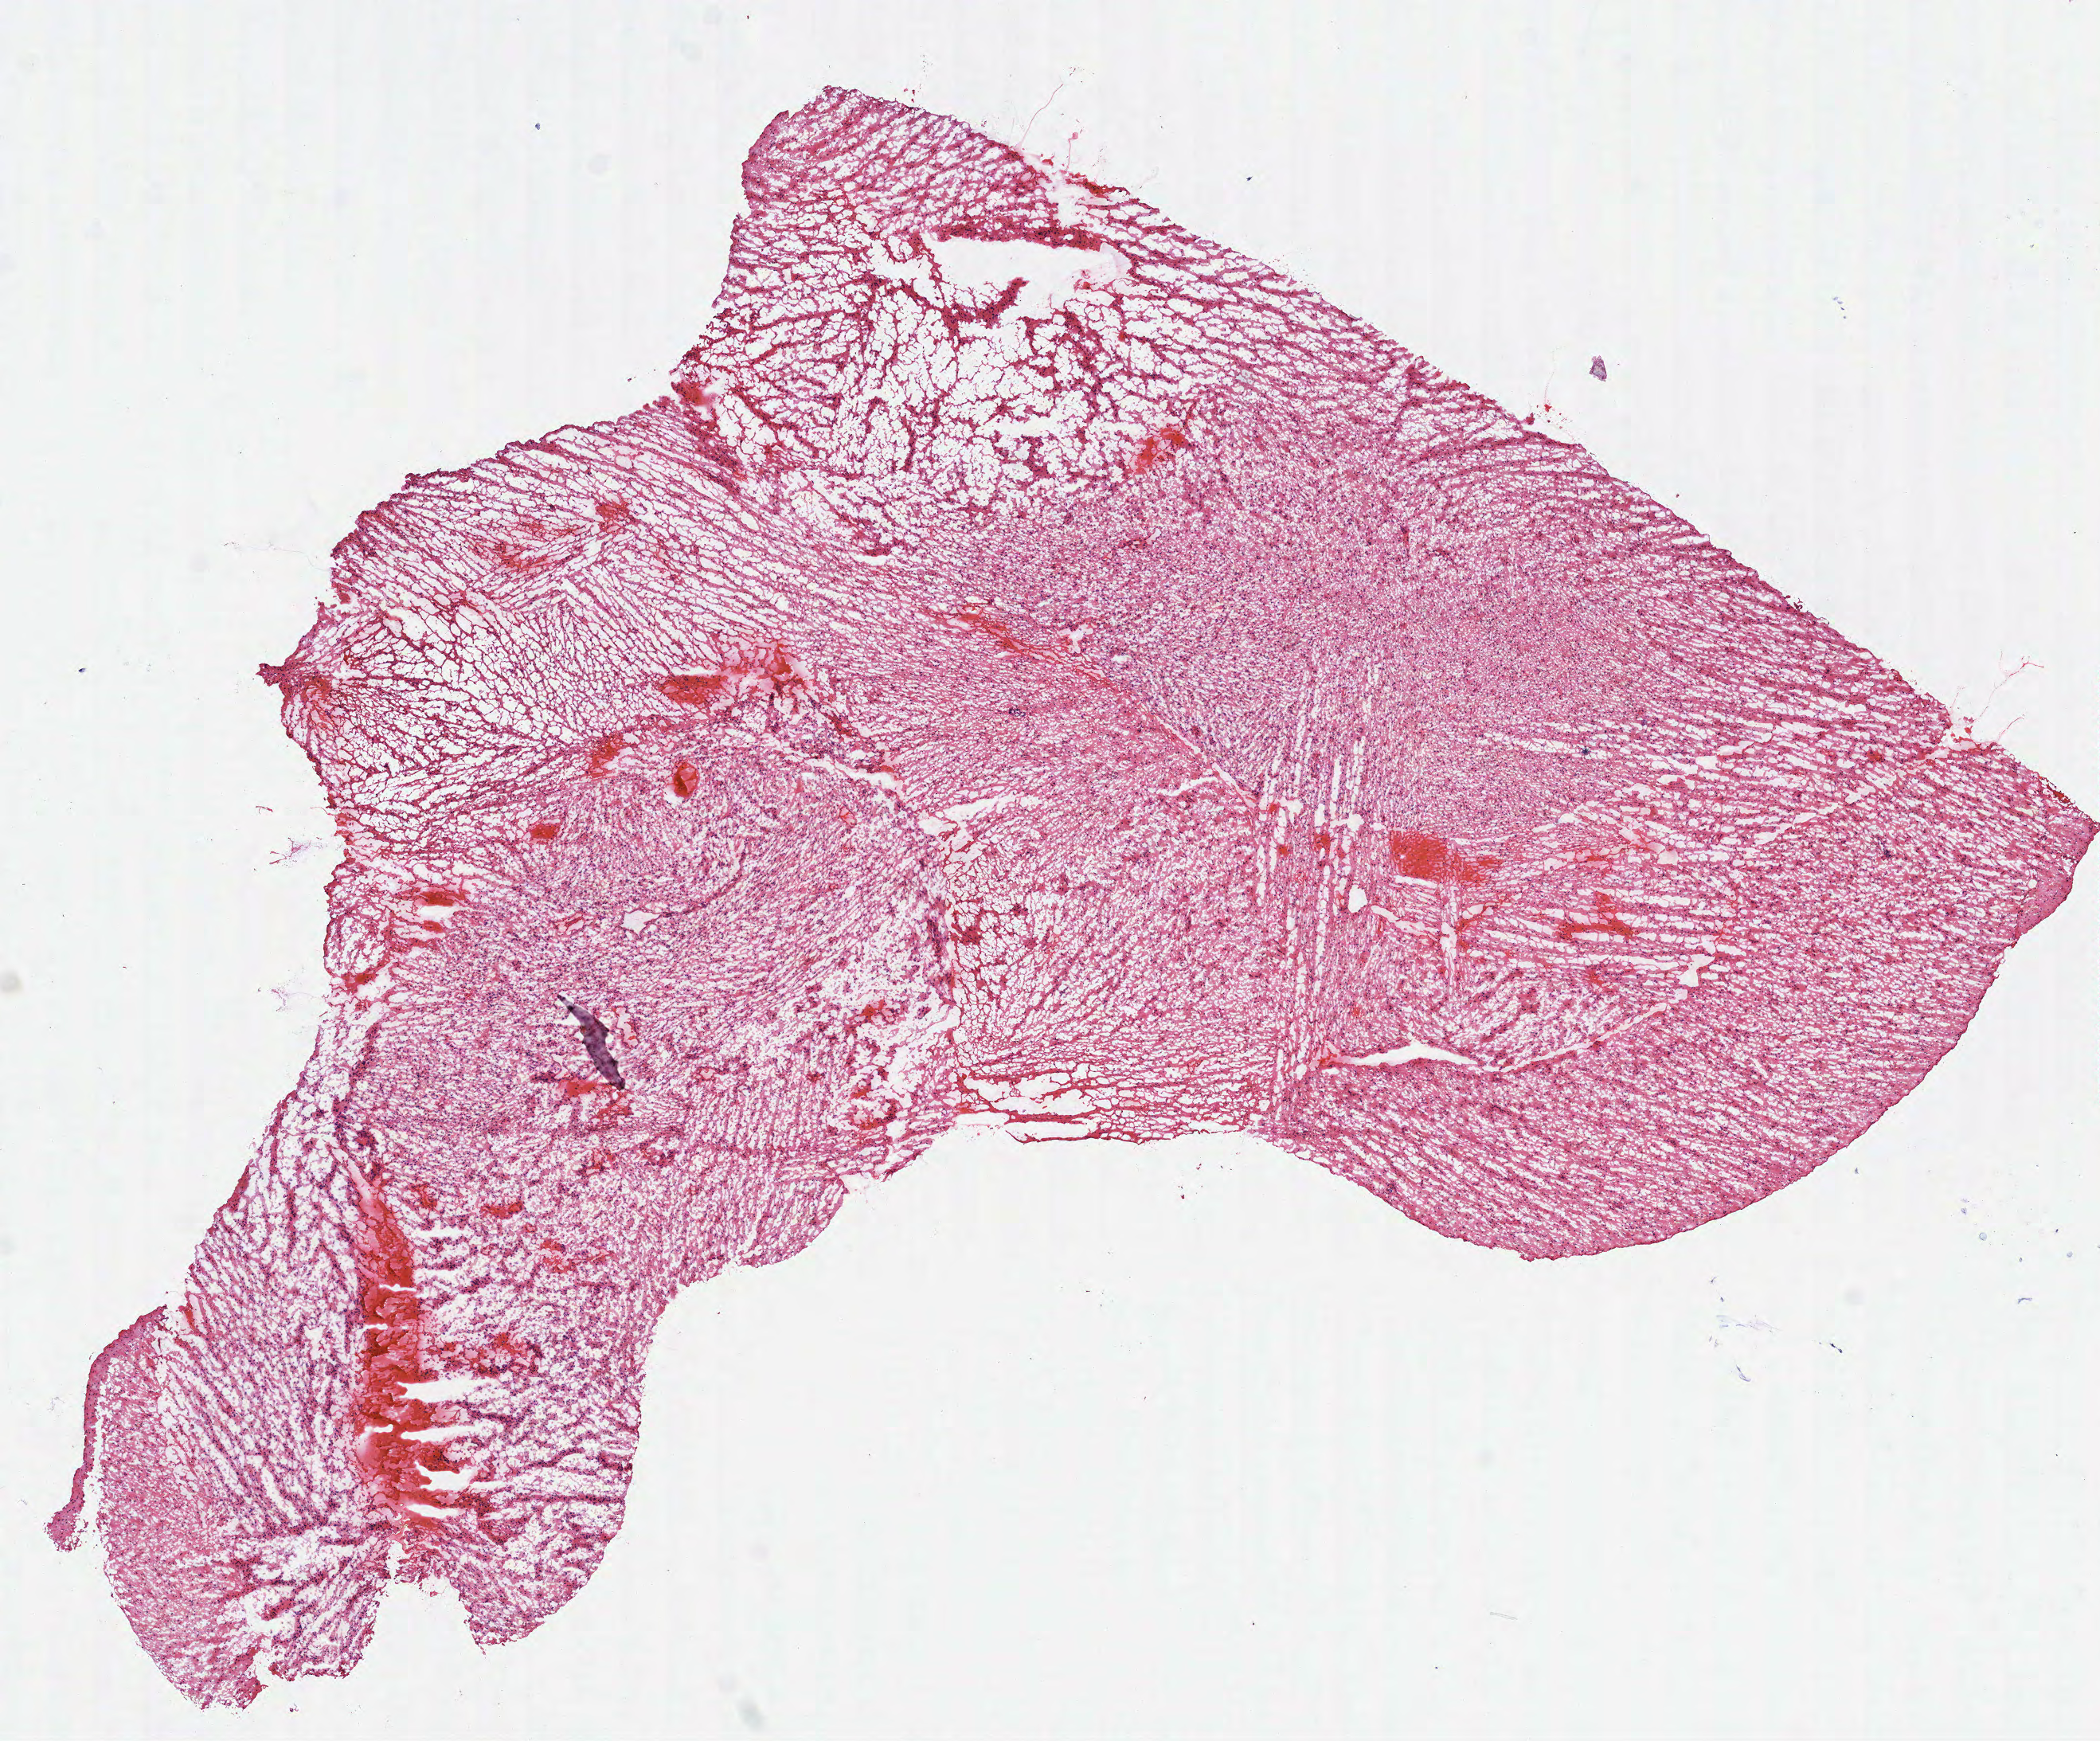
Whole-slide histology image, H&E, a low-resolution overview of the entire scanned area, about 10.6 x 8.8 mm. Frozen section. Primary tumour sample from the brain. Patient: male, age at initial diagnosis 48 years. Histologic grade: G3 (poorly differentiated). Pathologist review of this section (percent, as recorded): tumour cells 100%, tumour nuclei 70%, normal cells 0%, stromal cells 0%, necrosis 0%.
Histologic diagnosis: Astrocytoma, anaplastic. Laterality: right.